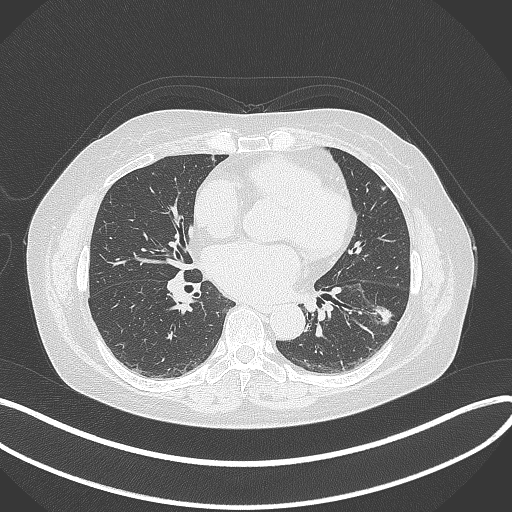
Chest CT, one axial slice; slice 166 of 373 in the series (ordered by position); reconstruction kernel B70f; 120 kVp; lung window (W 1500 / L -600 HU); 1 mm slice thickness; 512 × 512 image matrix. Female patient, age 67 years. From the clinical record (not read from this slice): clinical TNM (as recorded): T1c N0 M0; histopathological grade: G2.
Annotated regions visible in this slice (rectangle marked by the reading radiologist):
- lung tumour (recorded histology: adenocarcinoma): bounding box [x1, y1, x2, y2] px = [359, 293, 400, 329]